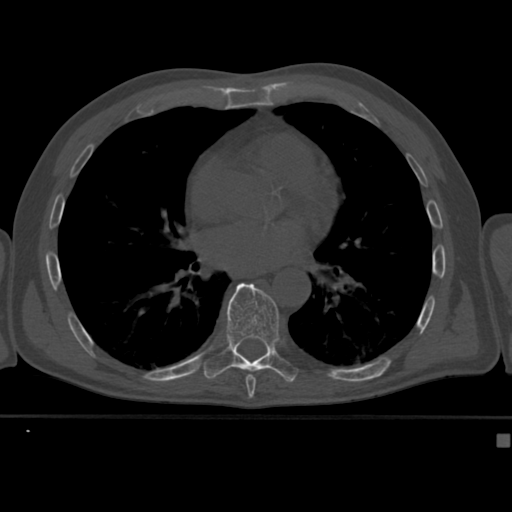
CT including the spine, one axial slice; position 250 of 430 along the scan axis; 120 kVp; bone window (W 1800 / L 400 HU); 1.5 mm slice thickness; 512 × 512 image matrix. Male patient, age 64 years. From the clinical record (not read from this slice): primary cancer: uterus.
Outlined on this slice (semi-automatically segmented with operator editing):
- T8 vertebra: bounding box (x1, y1, x2, y2) in pixels: (245, 374, 256, 382)
- T9 vertebra: (202, 283, 299, 382)